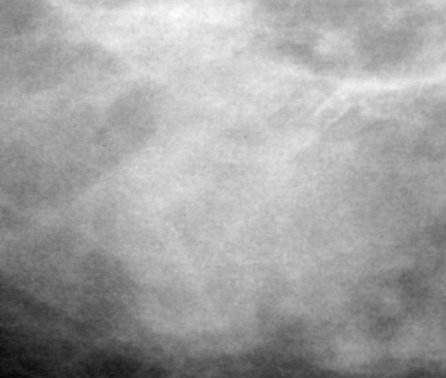
Cropped region of a digitized screen-film mammogram centred on a radiologist-marked abnormality; left breast; MLO view; BI-RADS breast density category 3 (scale 1–4).
- Finding: mass, shape round, margins ill defined; BI-RADS assessment category 4; pathology (as recorded): malignant.